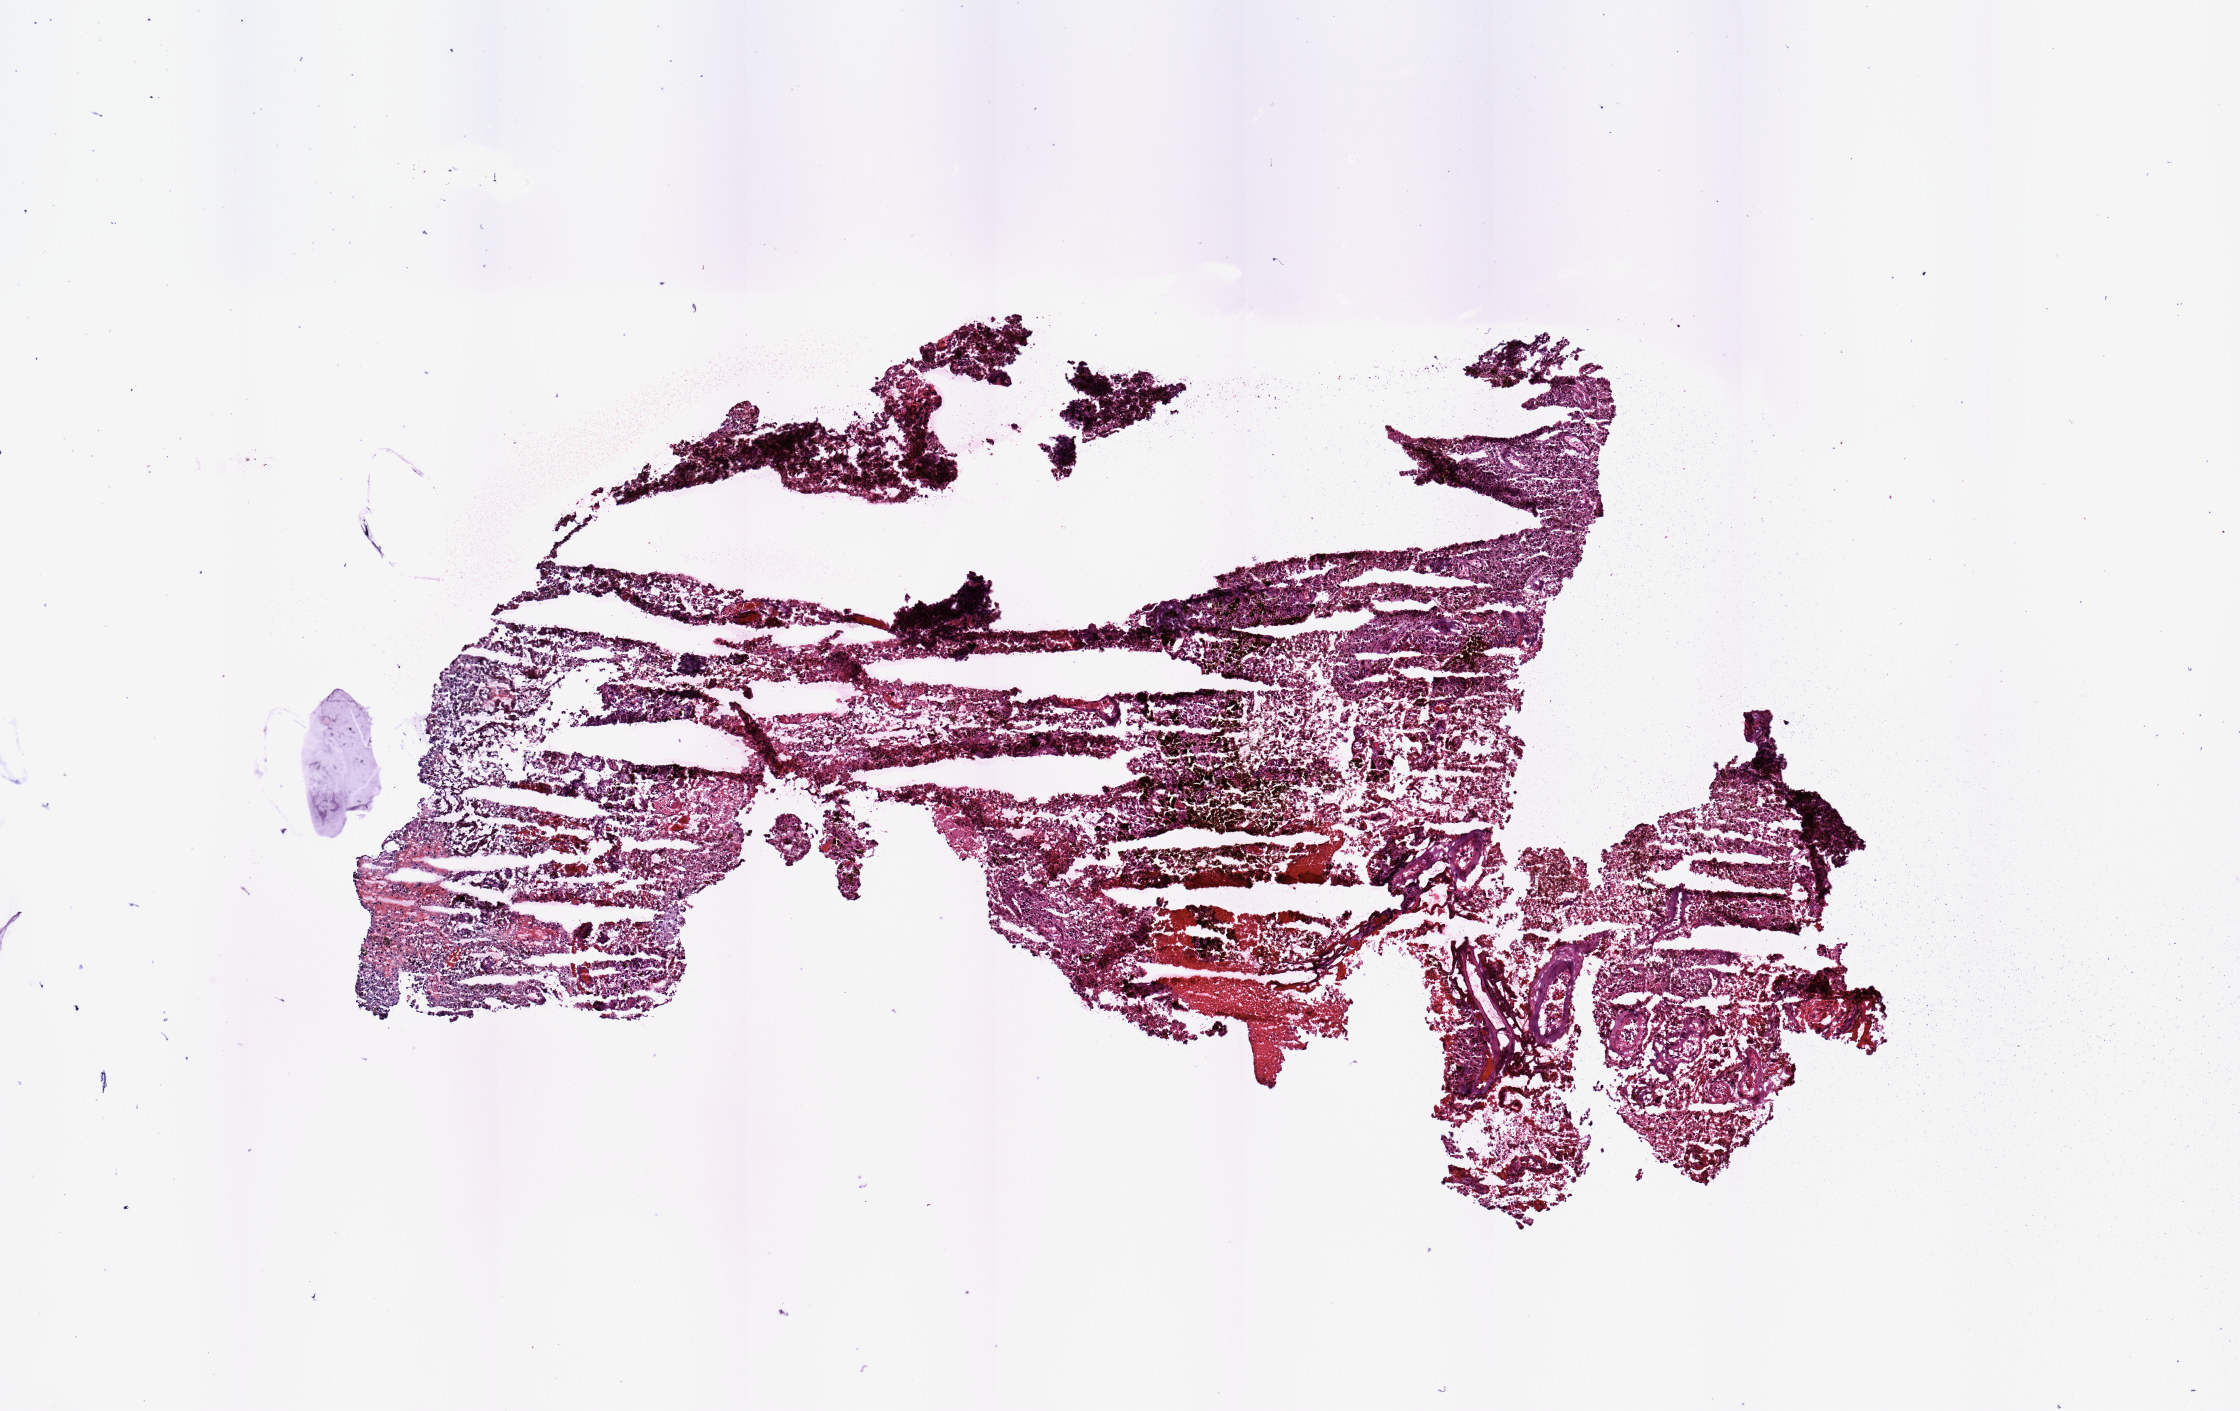
Digitized H&E tissue section (whole slide), shown as a low-resolution overview of the whole scanned area (about 8.9 x 5.6 mm, from a 20x scan), melanoma tumour tissue; sampled site not recorded. 75-year-old male patient.
- patient diagnosis (cohort enrolment): cutaneous melanoma (skin)
- primary tumour site (as recorded): head & neck